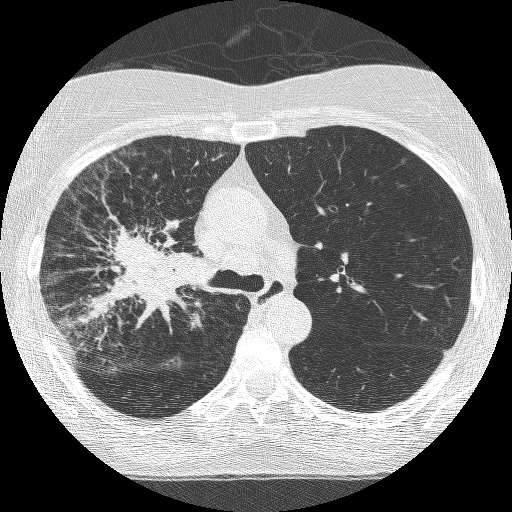
Axial slice from a low-dose chest CT screening exam; third screening round (two years after baseline); lung window (W 1500 / L -600 HU); 1.25 mm slice thickness; lung (sharp) reconstruction kernel (BONE); slice 173 of 253 in the series; 512 × 512 image matrix, field of view 294 × 294 mm. Female, age 64 years at enrolment. Former smoker at enrolment.
Lesion marked by an expert reader, bounding box (x1, y1, x2, y2) in pixels: (88, 218, 205, 335). The exam's reader record, not a measurement of the box and not confirmed to be the same lesion: non-calcified nodule or mass ≥4 mm, right upper lobe, 49 × 43 mm, spiculated (stellate) margins, soft tissue attenuation, pre-existing on the prior screen: yes; interval growth: yes. Official screen result: positive, other. Later outcome: lung cancer diagnosed 7 days after this screen — adenocarcinoma, NOS, right upper lobe, right middle lobe, right hilum, stage IV (AJCC 6th edition), 85 mm at pathology.